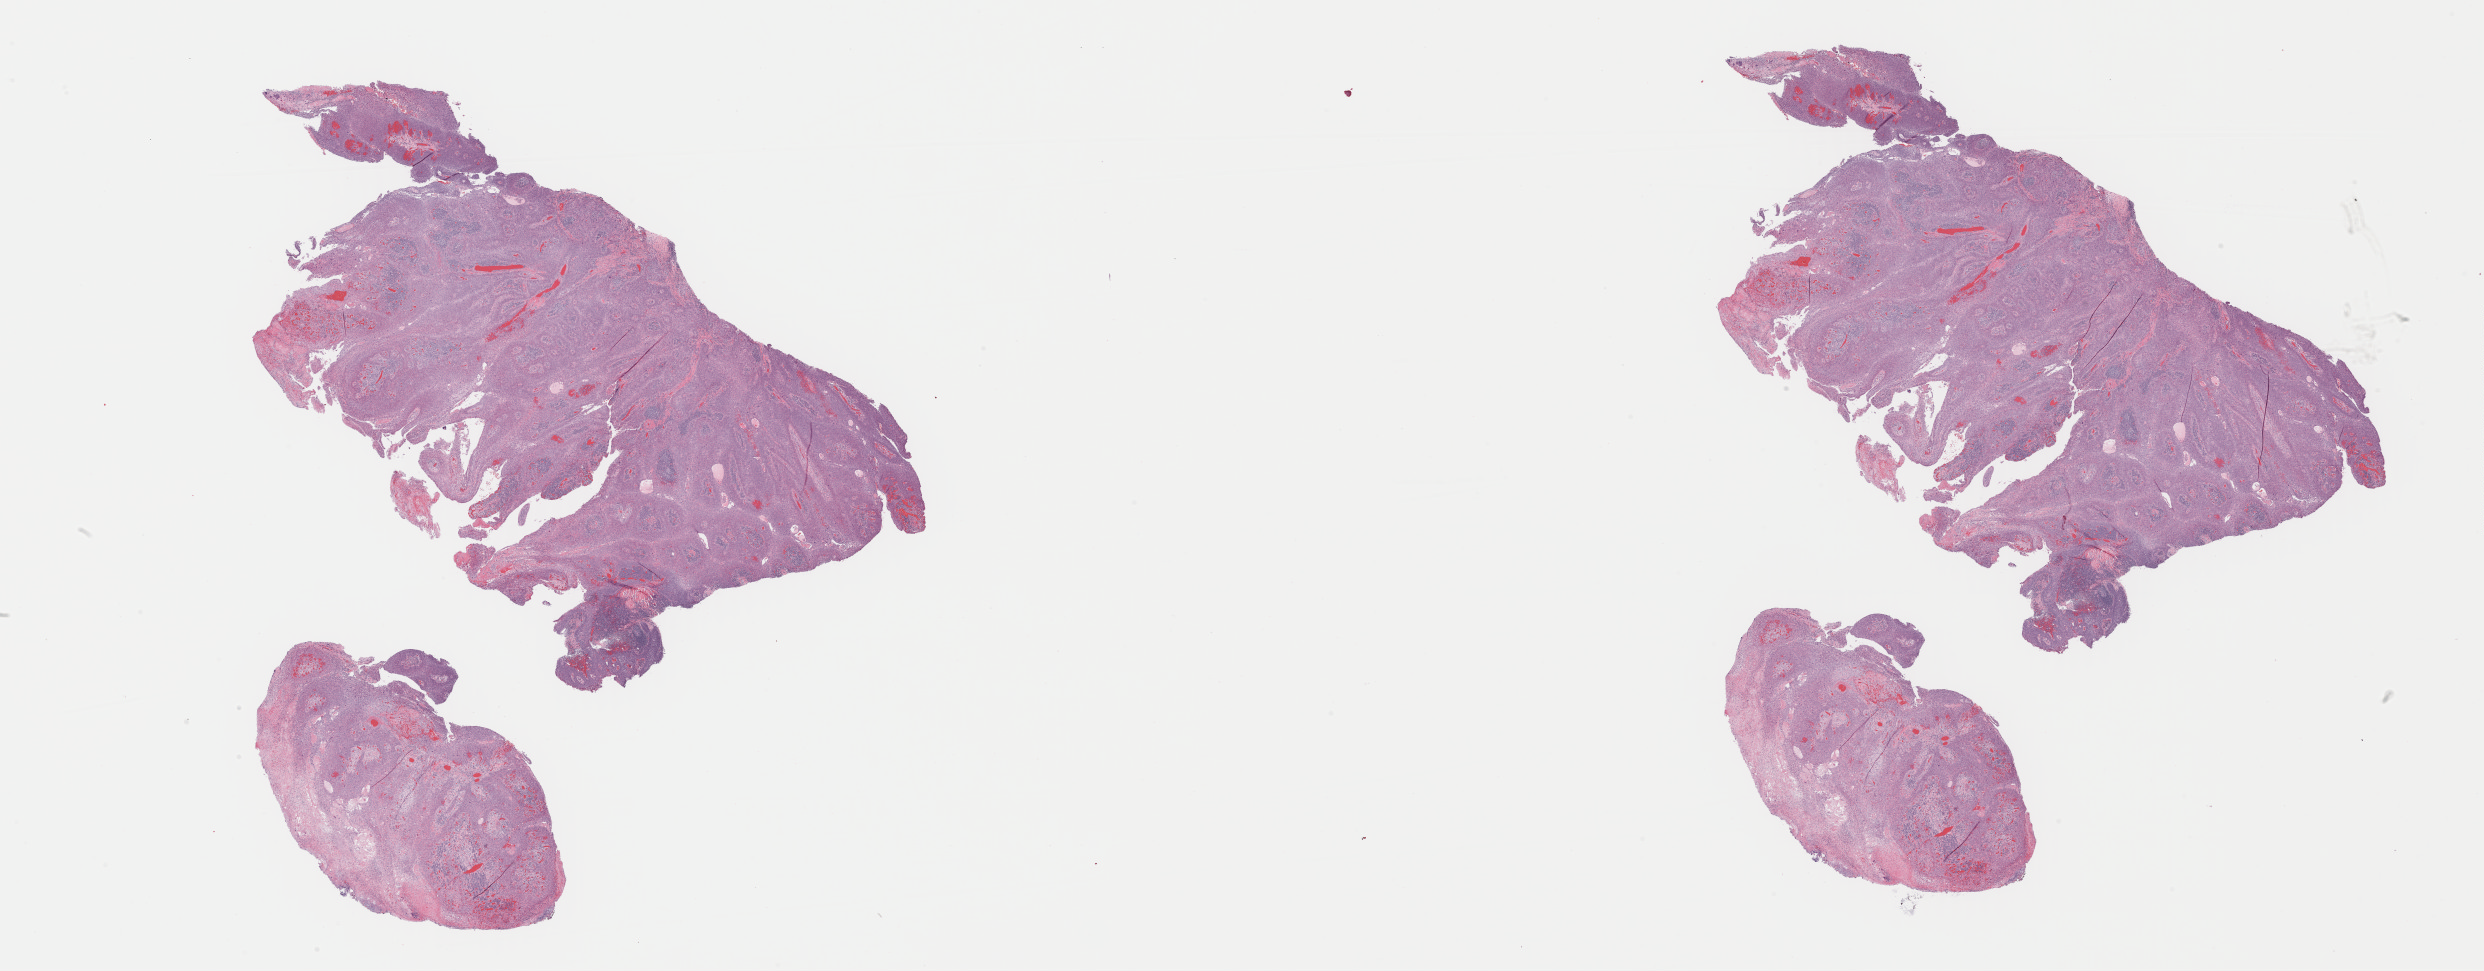
H&E whole-slide image — whole scanned area (about 39.2 x 15.3 mm) shown as a low-resolution overview. Formalin-fixed paraffin-embedded (FFPE) diagnostic section. Head and neck, primary tumour sample. Patient: male, age at initial diagnosis 46 years. Histologic grade: G2 (moderately differentiated).
Lymph nodes positive (case pathology): 0 of 35 examined. Diagnosis: Squamous cell carcinoma, NOS. Laterality: left. AJCC pathologic stage: II (7th edition).